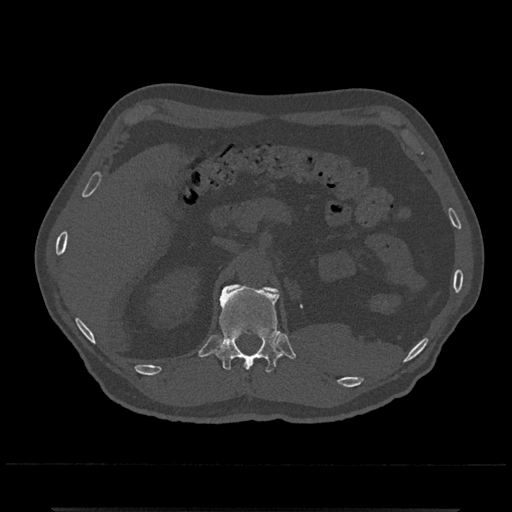
CT including the spine, one axial slice. Slice 428 of 797 in the series (ordered by position). Reconstruction kernel Br40s/3. 120 kVp. Bone window (W 1800 / L 400 HU). 0.5 mm slice thickness. 512 × 512 image matrix, field of view 393 × 393 mm. Male patient, age 67 years. Case-level facts recorded for this patient, not image findings: primary cancer: prostate.
Outlined on this slice (semi-automatic segmentation, software-assisted and operator-edited):
- L1 vertebra: bounding box [x1, y1, x2, y2] px = [260, 286, 271, 291]
- T12 vertebra: [214, 284, 282, 372]